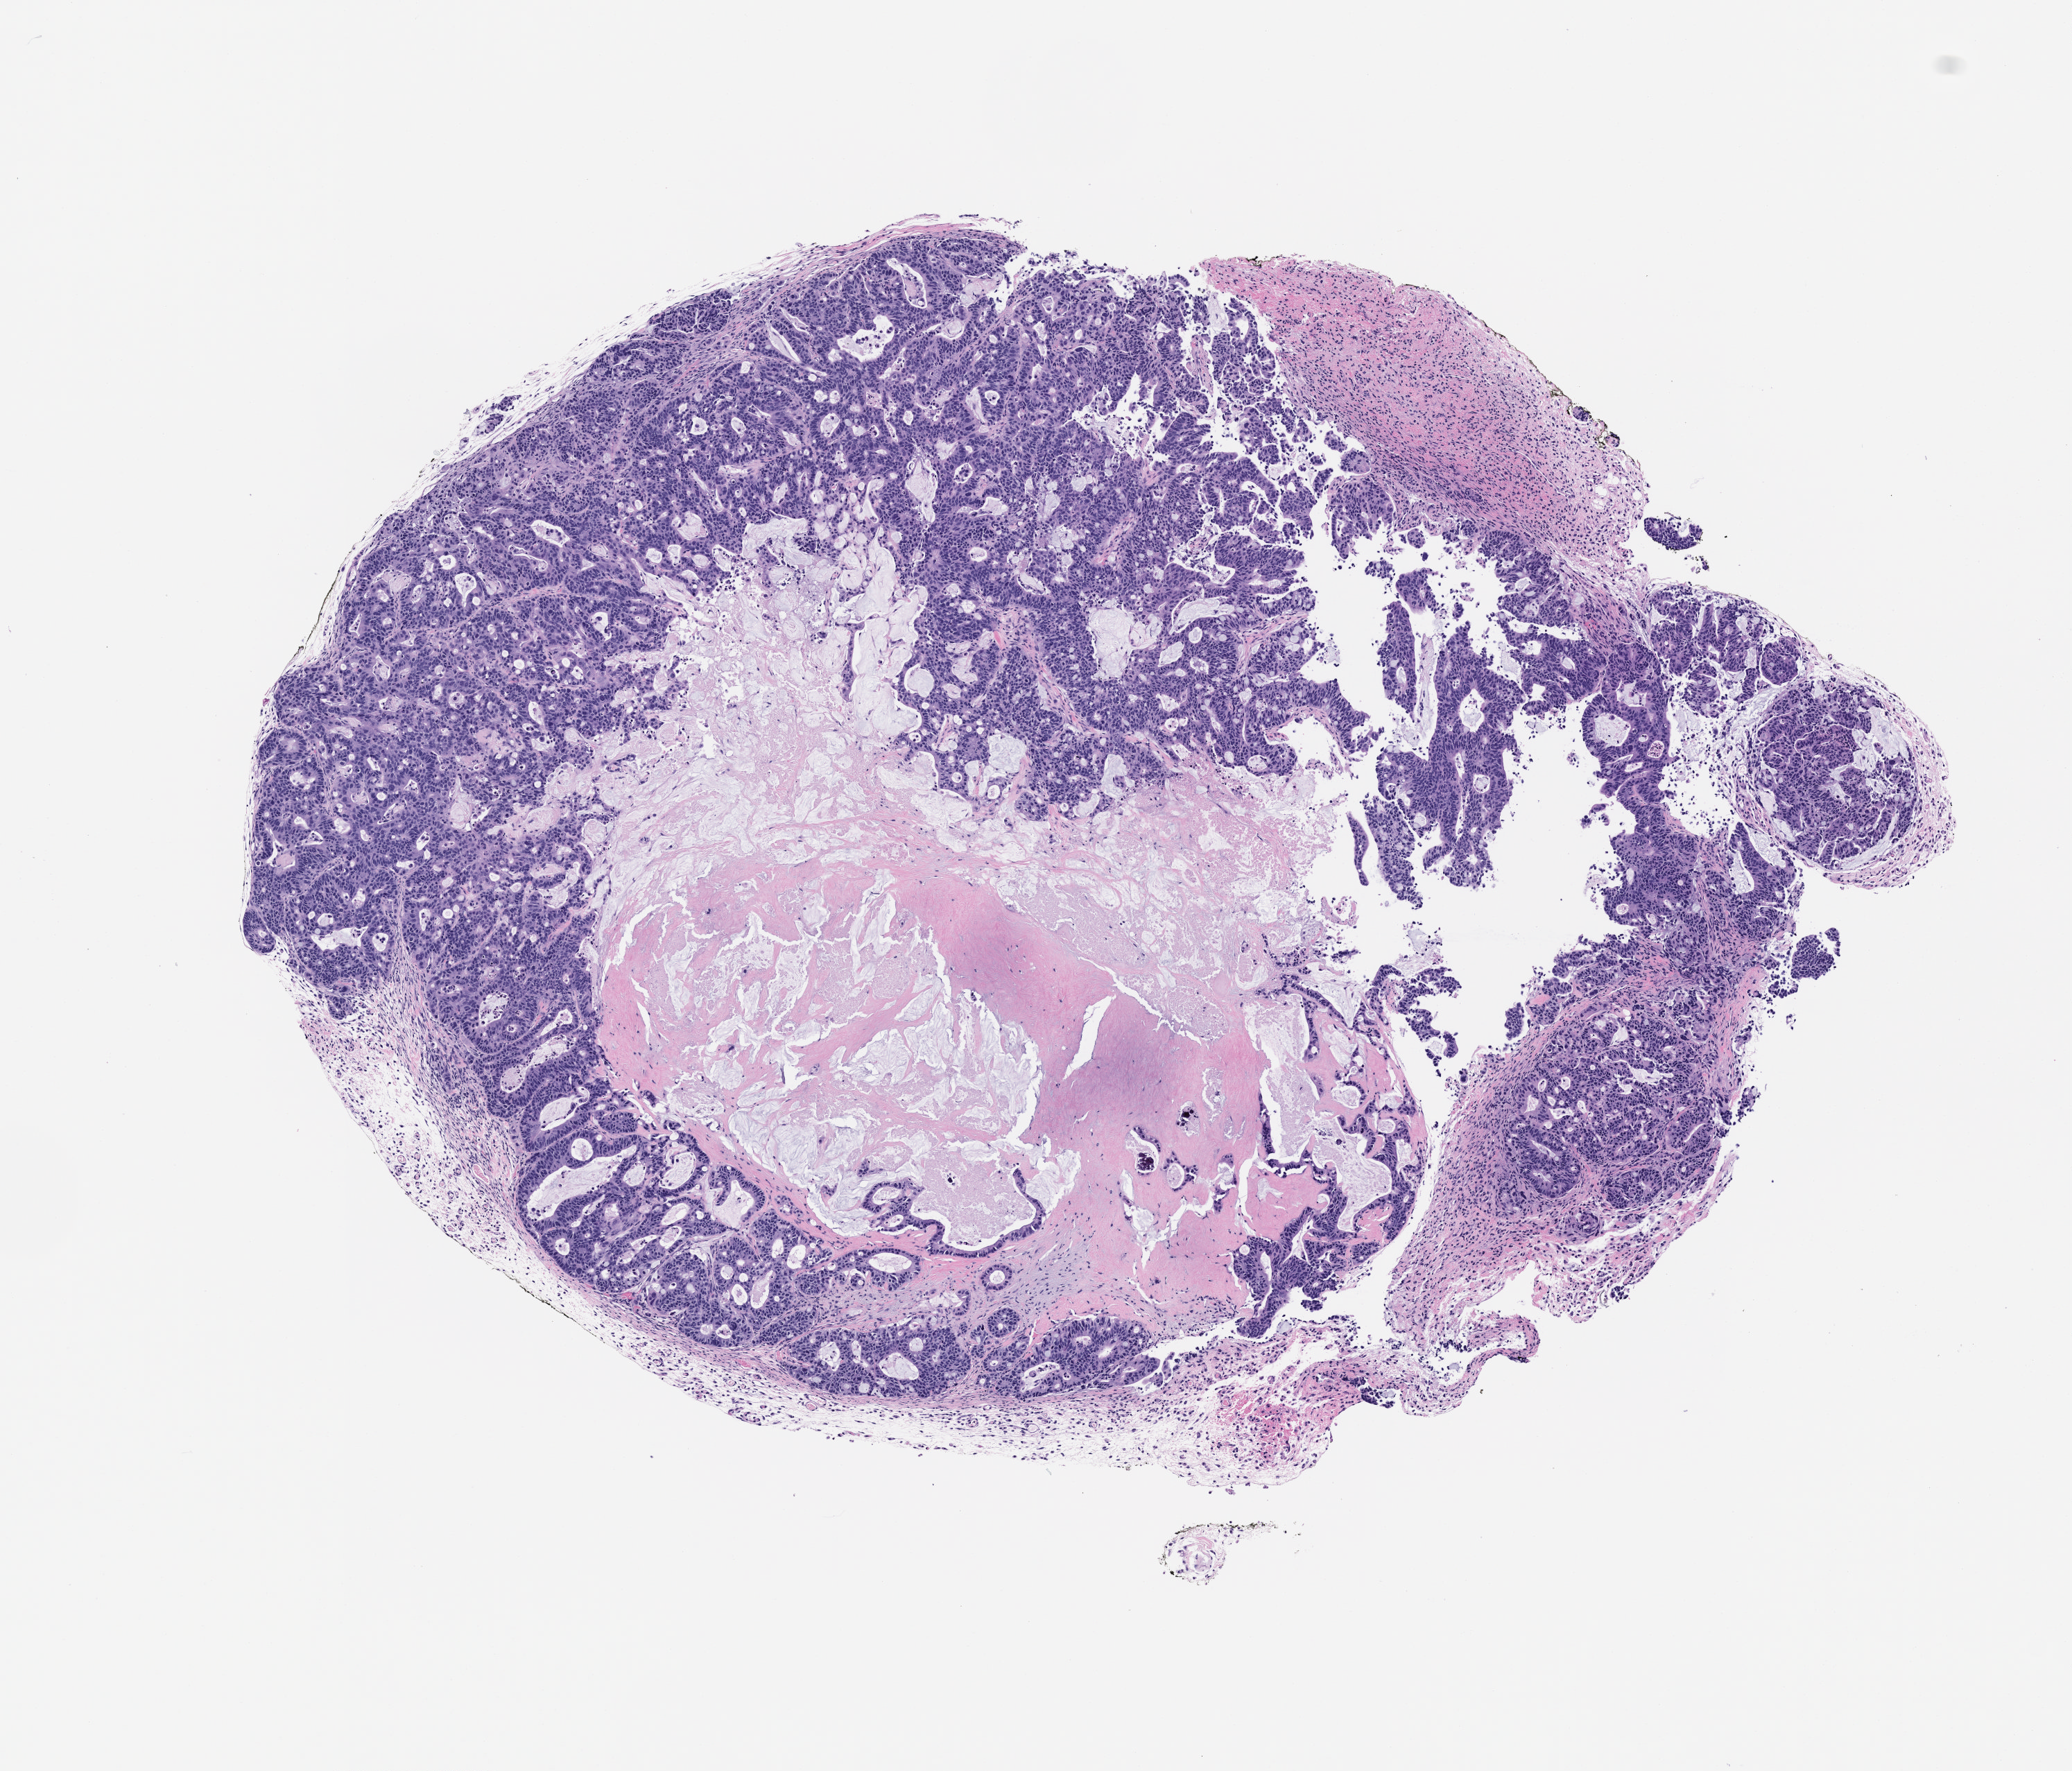
H&E whole-slide image of a patient-derived xenograft (PDX) tumor grown in a mouse, passage 0, whole scanned area (about 6.0 x 5.1 mm) shown as a low-resolution overview. FFPE section. Originating tumor site category: rectum.
• originating patient diagnosis: Rectal Adenocarcinoma